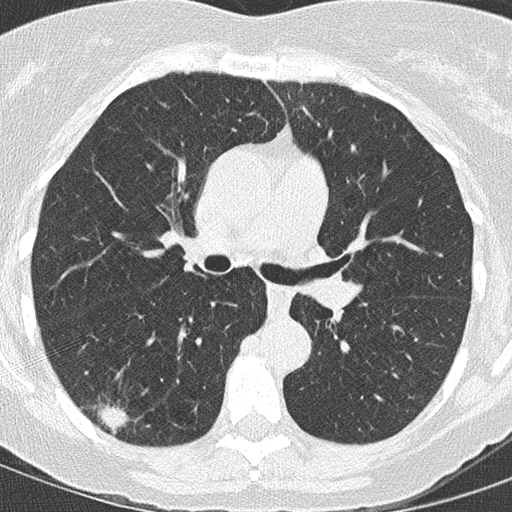
Low-dose screening chest CT, axial slice, baseline annual screen, lung window (W 1500 / L -600 HU), 2 mm slice thickness. Female, age 59 years at enrolment. Former smoker at enrolment.
- Expert-annotated lung lesion, bounding box [x1, y1, x2, y2] px = [69, 386, 146, 444].
- Reader record for this screening exam (exam-level; its link to the box is not recorded): non-calcified nodule or mass ≥4 mm, right lower lobe, 24 × 15 mm, spiculated (stellate) margins, soft tissue attenuation.
- Participant outcome: lung cancer diagnosed 12 days after this screen — adenocarcinoma, NOS, right lower lobe, moderately differentiated (G2), stage IIB (AJCC 6th edition), 22 mm at pathology.